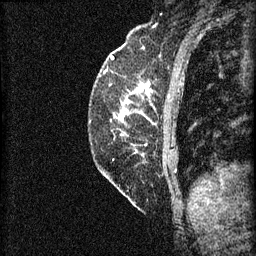
Breast MRI (dynamic contrast-enhanced), one sagittal slice; 3 images stored at this slice position (order not interpretable as contrast timing); 1.5 T; TE 4.2 ms, TR 8.2 ms; 256 × 256 image matrix, field of view 180 × 180 mm. Patient: female, 59 years.
Structures marked on this image (semi-automatically segmented with operator editing):
- analysis volume of interest (the breast-tissue region the enhancement analysis was run in; not a lesion): bounding box [x1, y1, x2, y2] px = [96, 74, 155, 125]
- tumour enhancement mask (voxels above the 70 % enhancement threshold inside the analysis volume of interest): [122, 84, 150, 105]